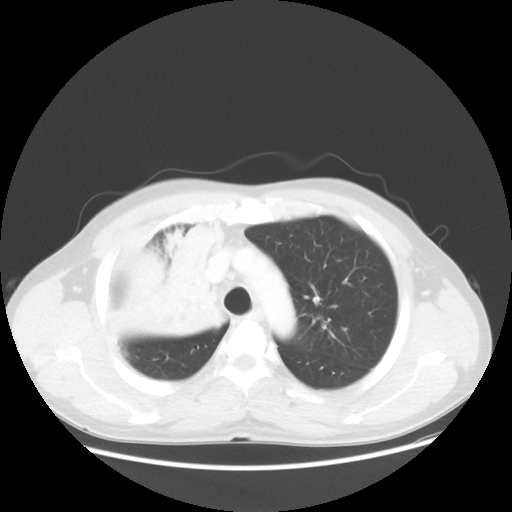
Chest CT, one axial slice. Position 41 of 56 along the scan axis. 100 kVp. Lung window (W 1500 / L -600 HU). 5 mm slice thickness. 512 × 512 image matrix. Male patient, age 60 years. Case-level facts recorded for this patient, not image findings: clinical TNM (as recorded): T2a N1 M0.
Structures marked on this image (rectangle marked by the reading radiologist):
- lung tumour (recorded histology: squamous cell carcinoma): bounding box [x1, y1, x2, y2] px = [102, 224, 221, 355]